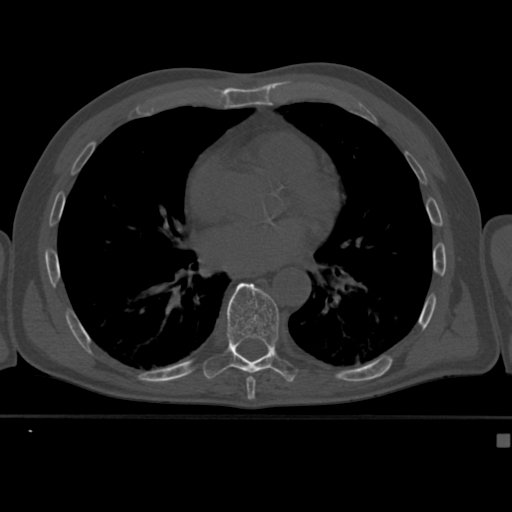
CT including the spine, one axial slice; position 249 of 430 along the scan axis; bone window (W 1800 / L 400 HU); 1.5 mm slice thickness; 512 × 512 image matrix, field of view 337 × 337 mm. Male patient, age 64 years. Case-level facts recorded for this patient, not image findings: primary cancer: uterus; vertebrae with lytic lesions (as recorded): T1, T4, T5, T7, L5.
Structures marked on this image (semi-automatically segmented with operator editing):
- T8 vertebra: bounding box <246,376,255,382> (left, top, right, bottom; pixels)
- T9 vertebra: <203,283,297,382>